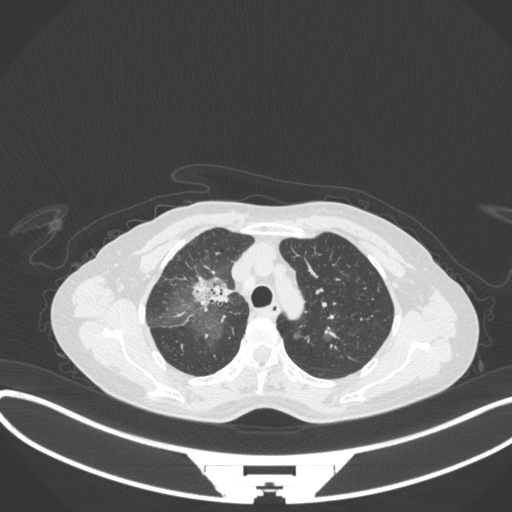
Chest CT, one axial slice. Slice 240 of 311 in the series (ordered by position). Reconstruction kernel B31f. 120 kVp. Lung window (W 1500 / L -600 HU). 1 mm slice thickness. 512 × 512 image matrix, field of view 400 × 400 mm. Female patient, age 59 years. From the clinical record (not read from this slice): clinical TNM (as recorded): T3 N0 M0.
Annotated regions visible in this slice (bounding box drawn by a radiologist):
- lung tumour (recorded histology: adenocarcinoma): box from (x=185, y=270) to (x=234, y=311) px